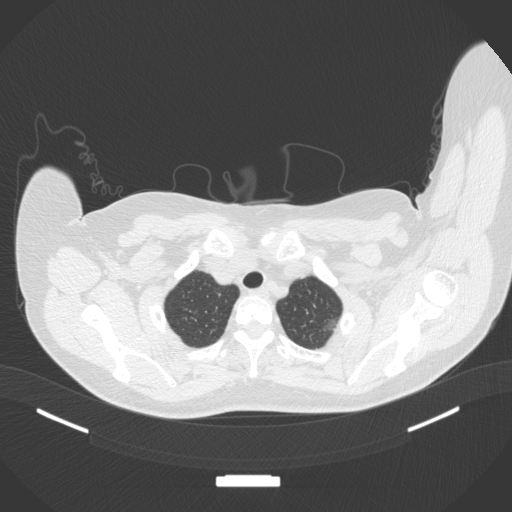
Chest CT, one axial slice. Position 329 of 386 along the scan axis. 120 kVp. Lung window (W 1500 / L -600 HU). 512 × 512 image matrix. Patient: female, 58 years. From the clinical record (not read from this slice): clinical TNM (as recorded): T1c N0 M0.
Structures marked on this image (bounding box drawn by a radiologist):
- lung tumour (recorded histology: adenocarcinoma): box from (x=319, y=314) to (x=345, y=339) px